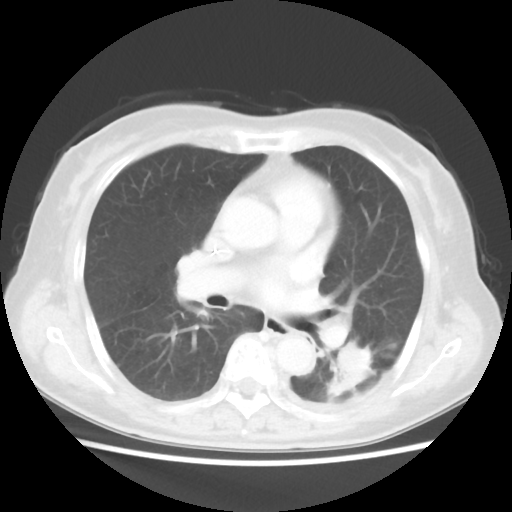
Chest CT, one axial slice. Position 20 of 40 along the scan axis. 100 kVp. Lung window (W 1500 / L -600 HU). 512 × 512 image matrix. Patient: female, 69 years. From the clinical record (not read from this slice): clinical TNM (as recorded): T1c N0 M0.
Outlined on this slice (rectangle marked by the reading radiologist):
- lung tumour (recorded histology: adenocarcinoma): bounding box [x1, y1, x2, y2] px = [325, 344, 376, 401]